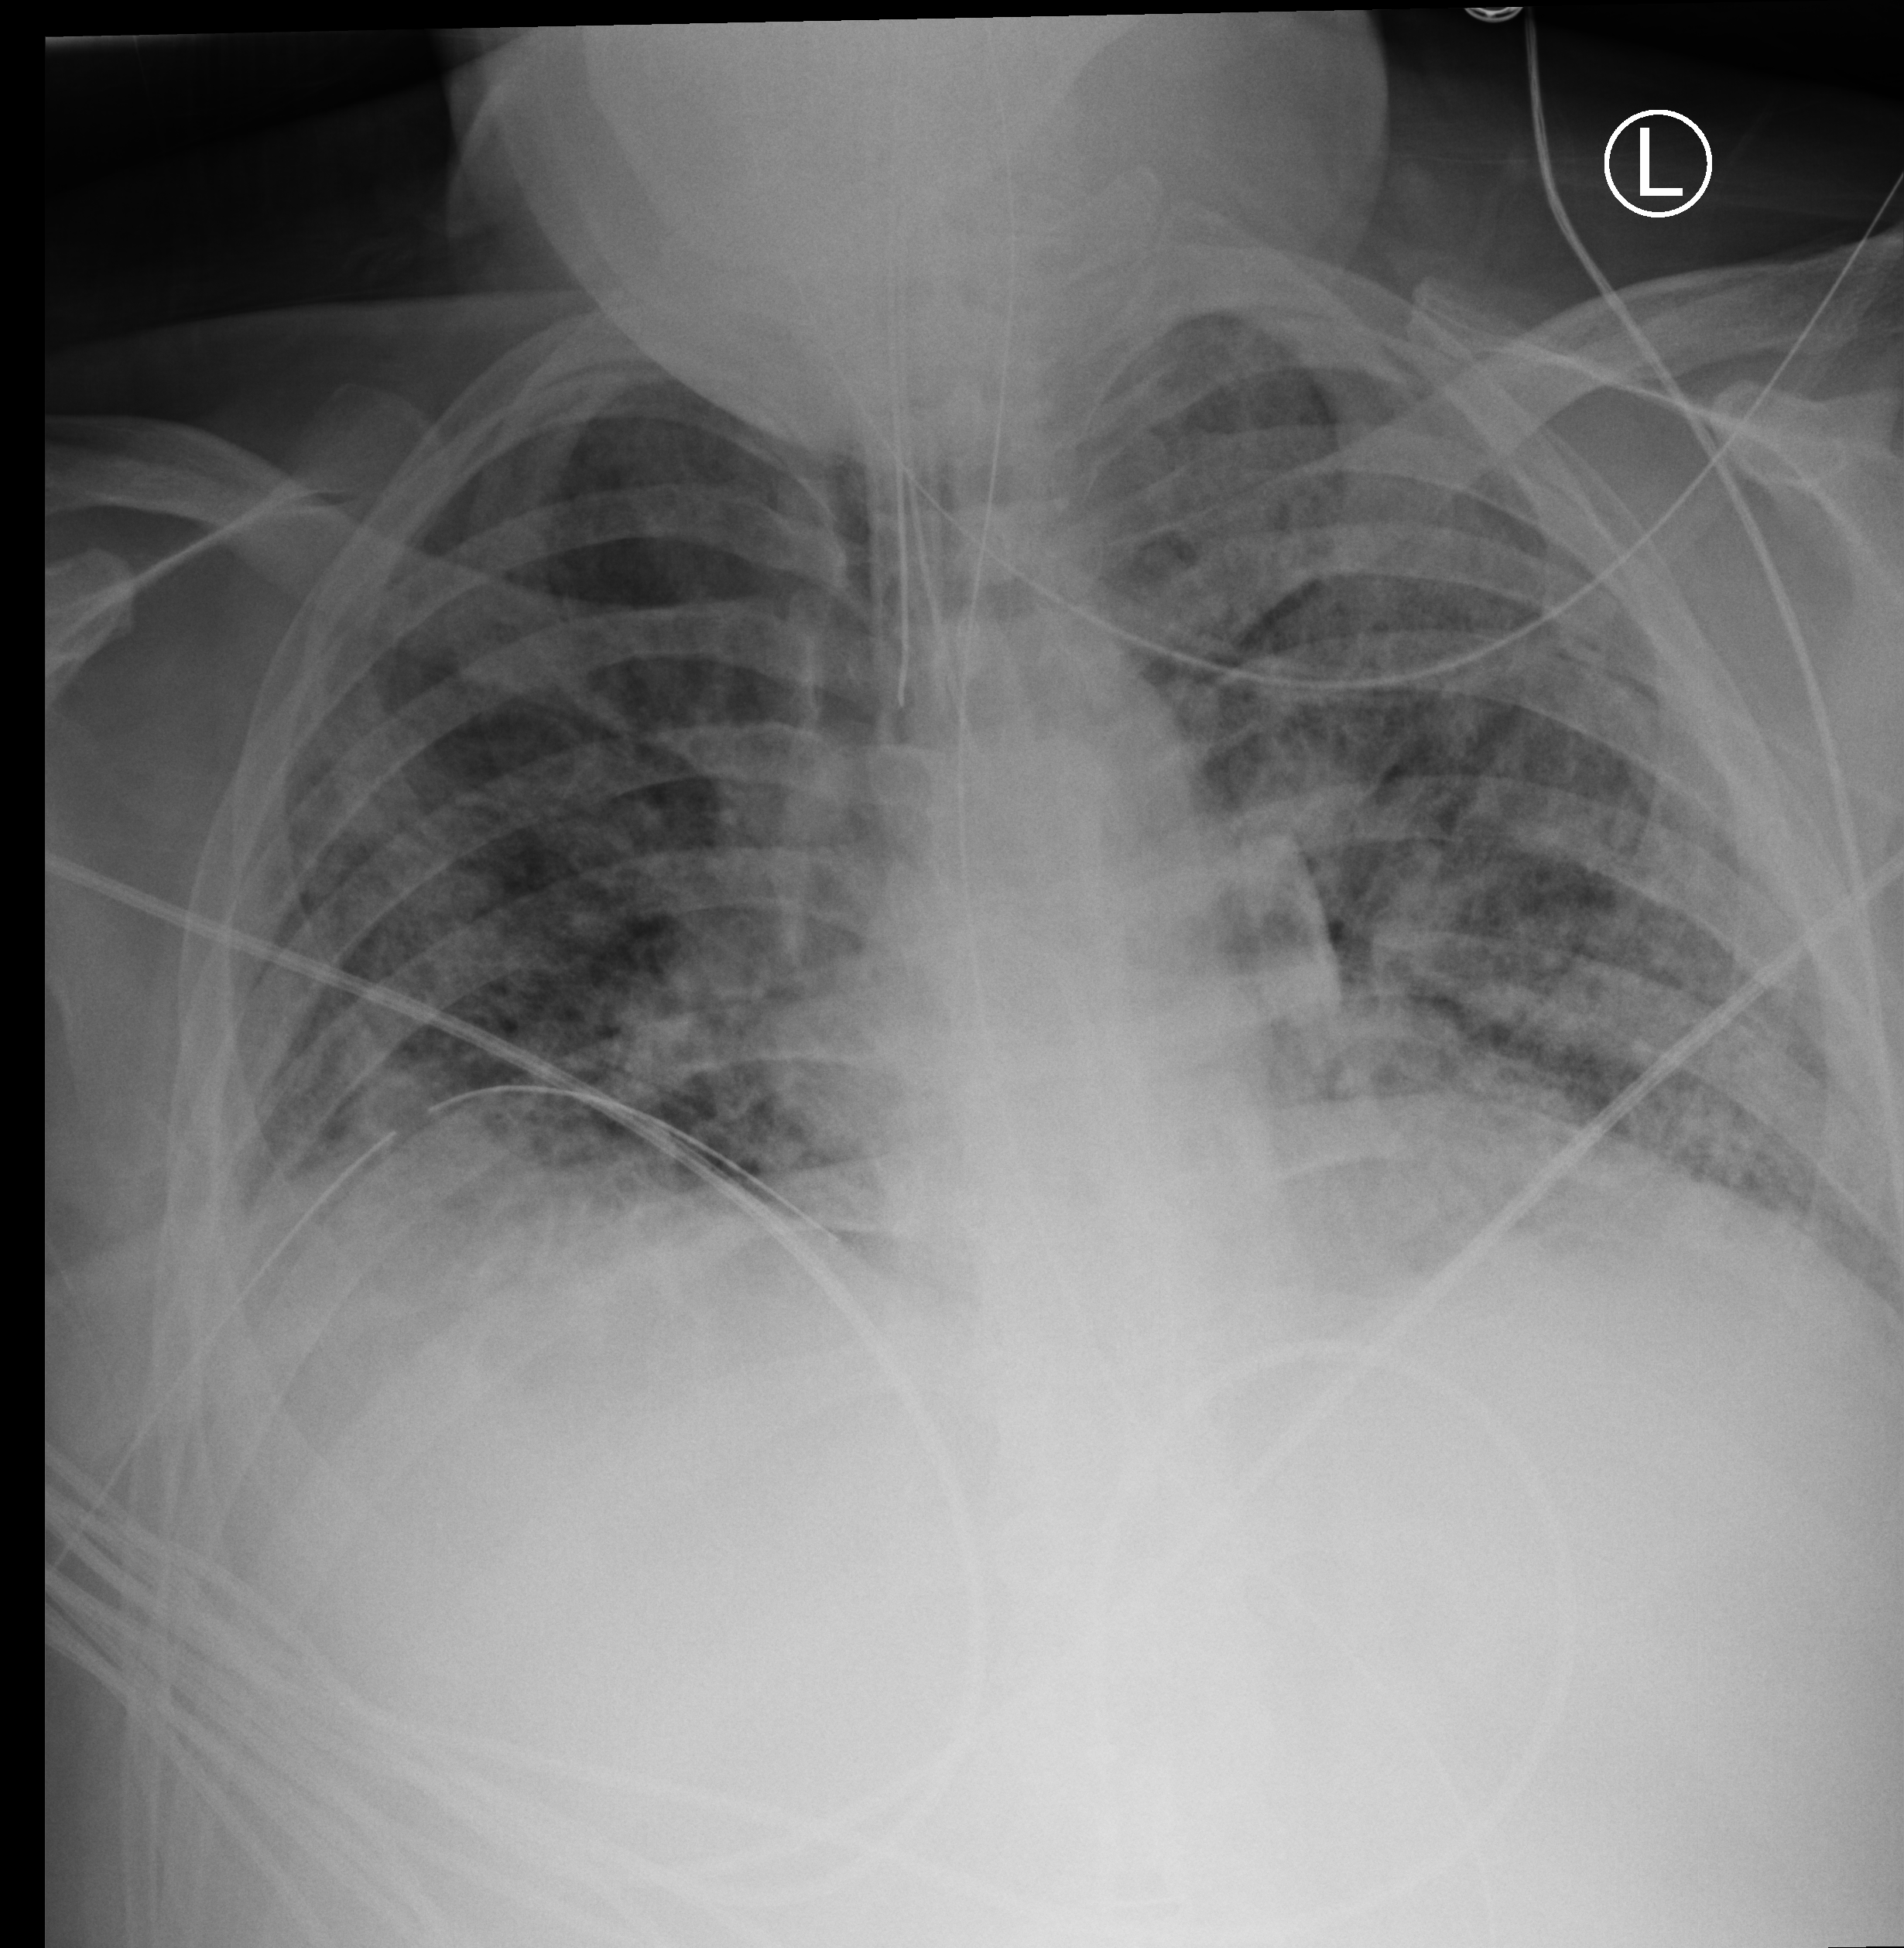
Chest X-ray (portable), anteroposterior (AP) projection. Patient hospitalised with COVID-19; male, aged 18–59 years.
Hospital-stay facts (about this admission, not read from this image; timing relative to this image not recorded): admitted to intensive care during this hospital stay: yes.